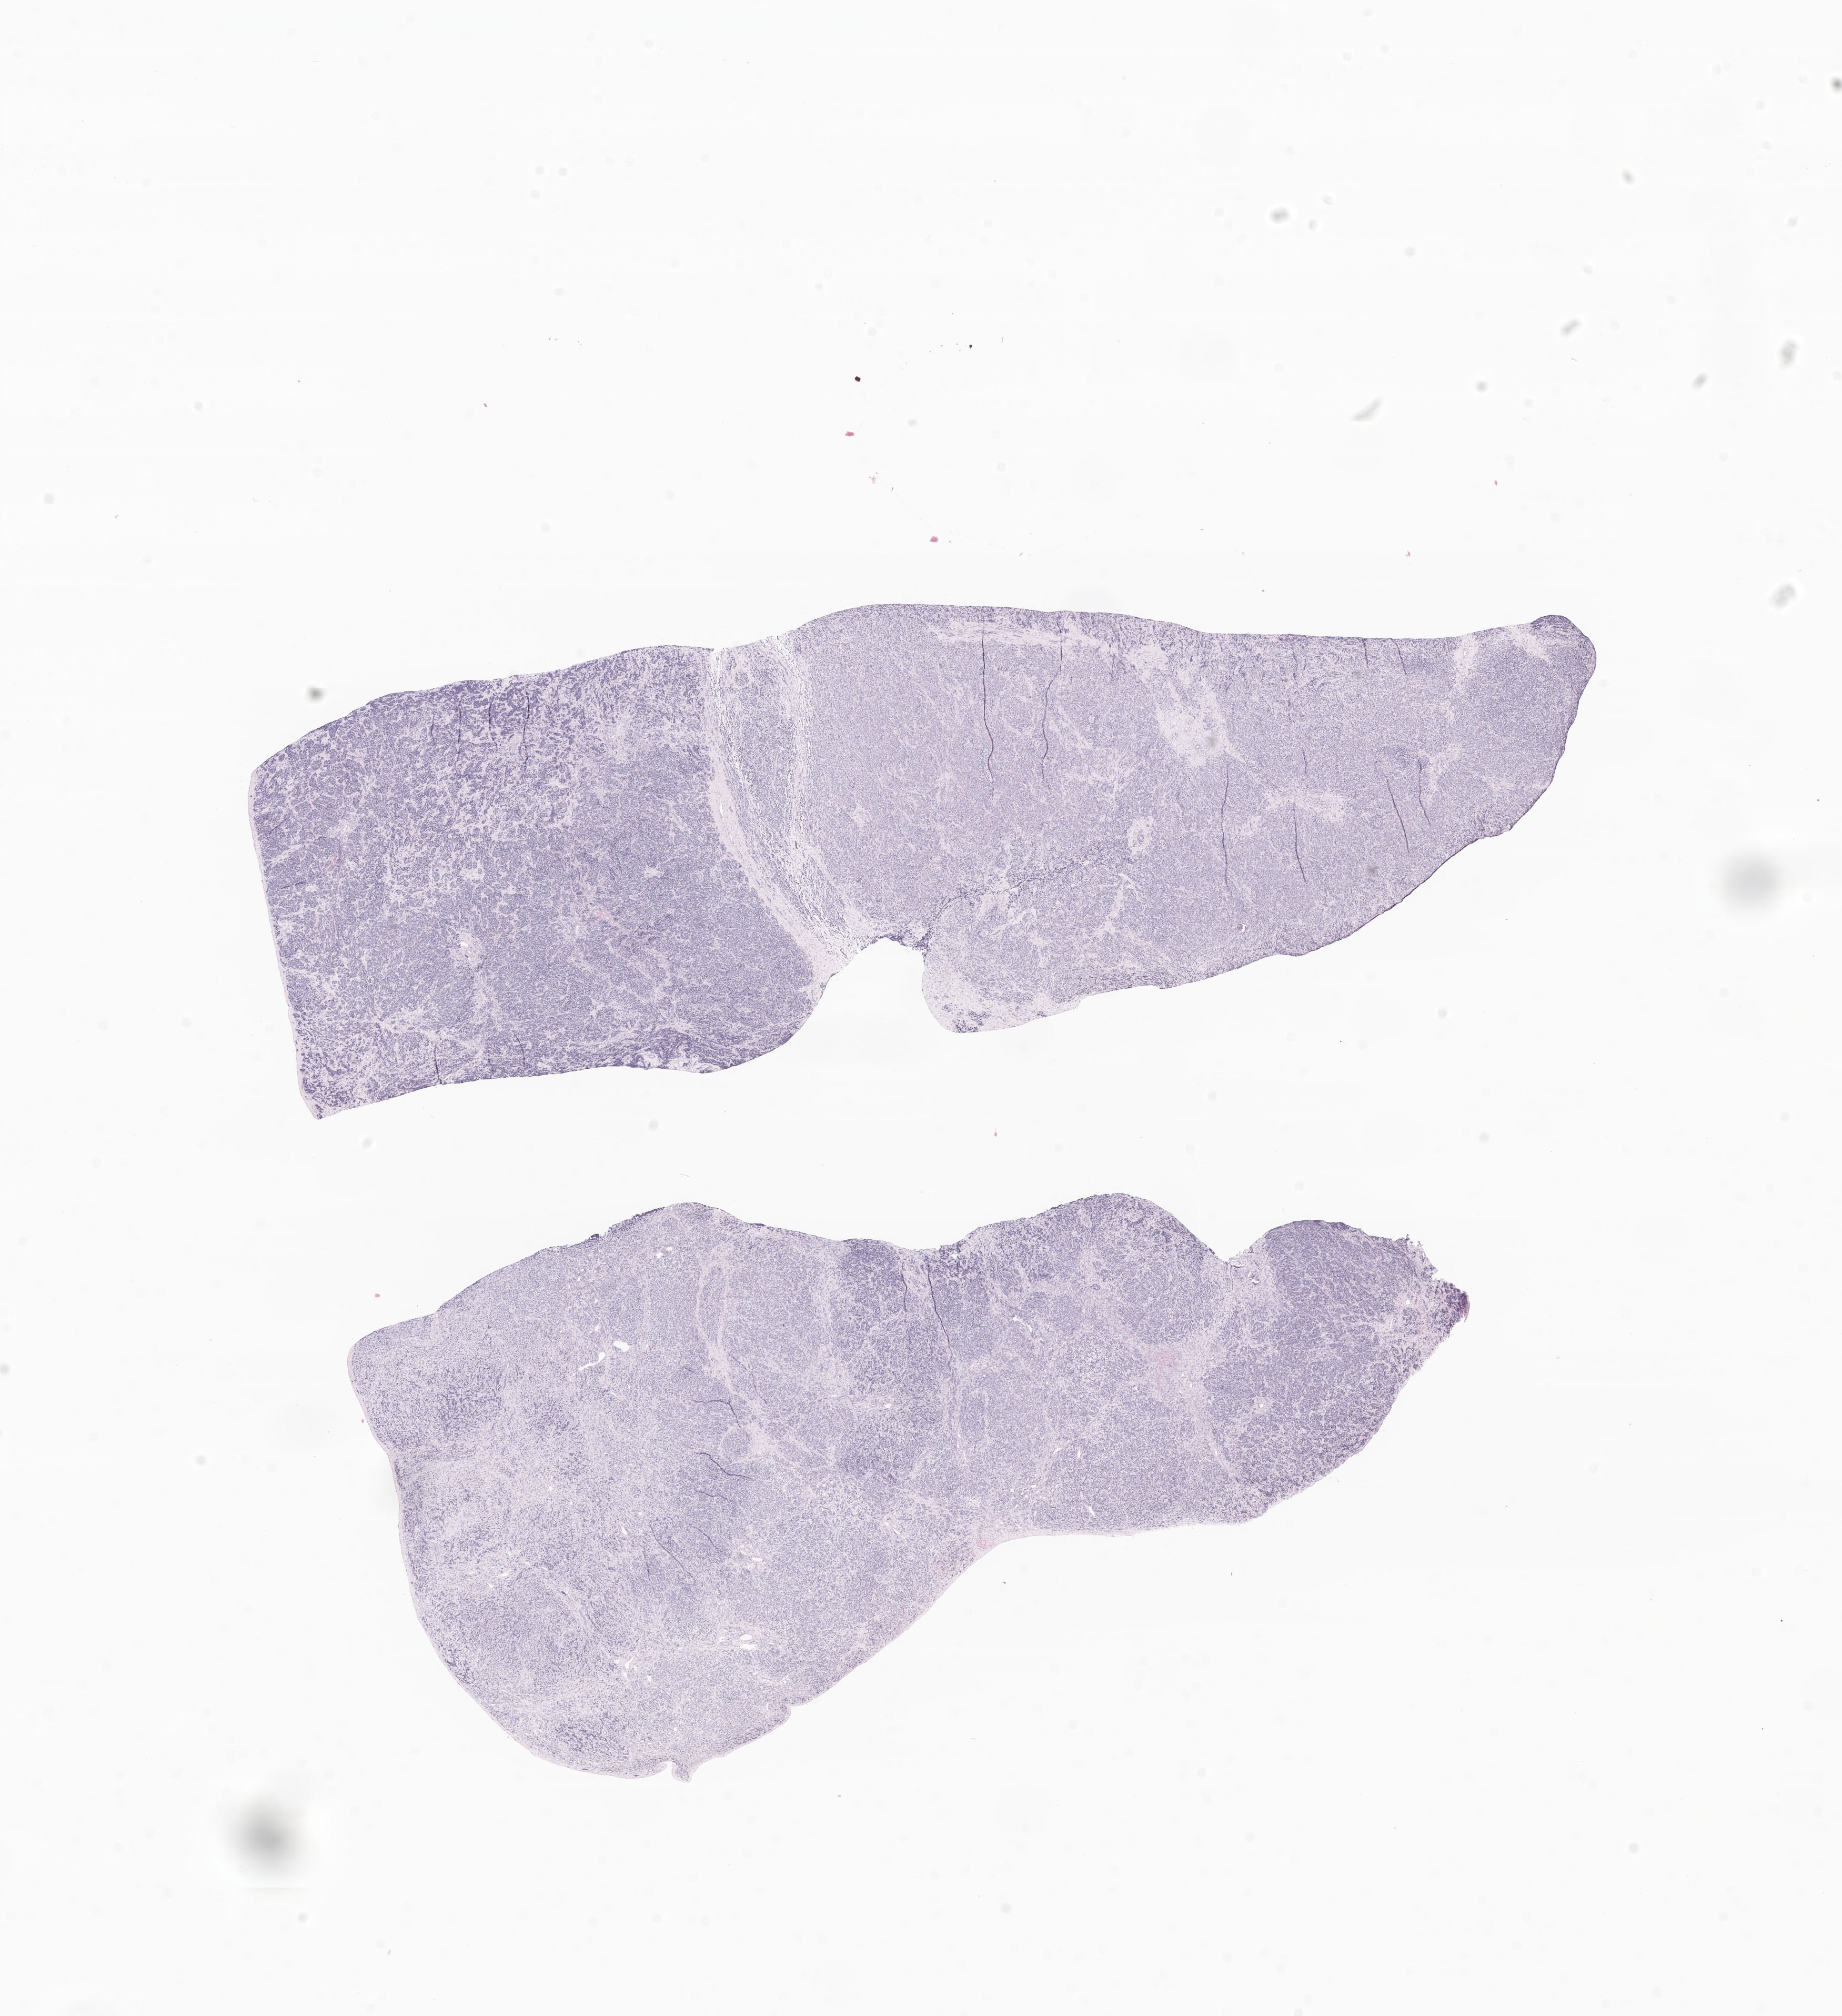
Whole-slide image, haematoxylin and eosin stain of tumor tissue from the adrenal gland — low-resolution overview of the scanned area, about 14.8 x 16.2 mm; FFPE section. Patient: female, age 164 days.
Diagnosis: Neuroblastoma, NOS.